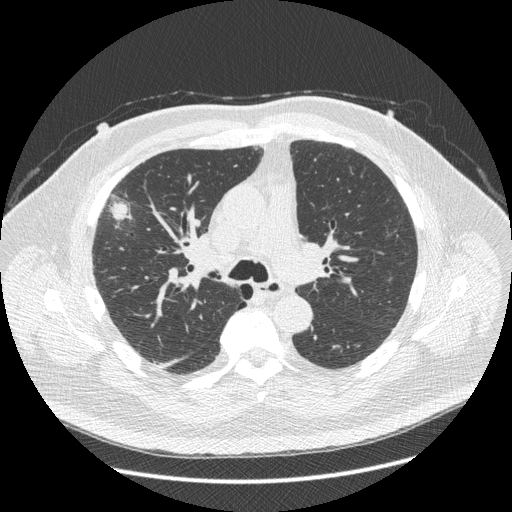
Low-dose screening chest CT, one axial slice. Position 272 of 426 along the scan axis. Reconstruction kernel STANDARD. 120 kVp. Lung window (W 1500 / L -600 HU). 1.25 mm slice thickness. 512 × 512 image matrix.
Annotated regions visible in this slice (expert manual segmentation):
- lesion 1 (tumor, upper lobe of right lung): bounding box (x1, y1, x2, y2) in pixels: (111, 203, 128, 215)